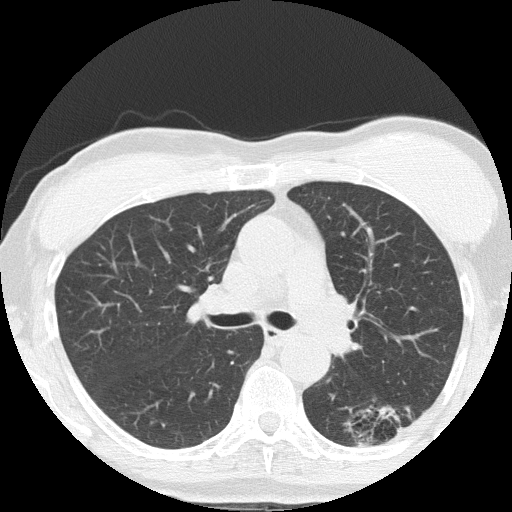
Chest CT (low-dose screening protocol), one axial image, third screening round (two years after baseline), lung window (W 1500 / L -600 HU), 2 mm slice thickness, 120 kVp, slice 59 of 152 in the series, 512 × 512 image matrix, field of view 308 × 308 mm. Female participant, aged 64 years at enrolment. Former smoker at enrolment.
• Expert reader's lesion annotation, bounding box <349,384,436,454> (left, top, right, bottom; pixels).
• The screening reader recorded 3 non-calcified nodules or masses ≥4 mm on this exam; which of them this box marks is not recorded.
• Official screen result: positive, other.
• Participant outcome: lung cancer diagnosed 212 days after this screen — adenocarcinoma, NOS, left lower lobe, moderately differentiated (G2), stage IA (AJCC 6th edition), 17 mm at pathology.